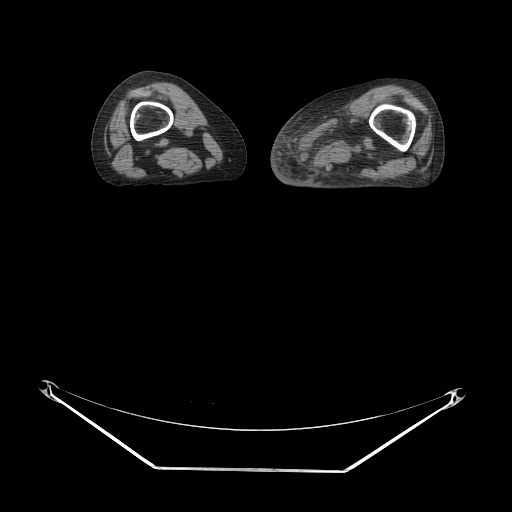
CT of an extremity soft-tissue mass (from a PET/CT study), one axial slice; reconstruction kernel STANDARD; 140 kVp; soft-tissue window (W 400 / L 40 HU); 3.75 mm slice thickness; 512 × 512 image matrix, field of view 500 × 500 mm. Female patient. From the clinical record (not read from this slice): histological type: pleomorphic leiomyosarcoma; grade: high; site of the primary tumour: left thigh.
Outlined on this slice (expert contour drawn on MRI and transferred to this co-registered scan by the dataset authors):
- gross tumour volume including surrounding oedema: bounding box <306,105,380,181> (left, top, right, bottom; pixels)